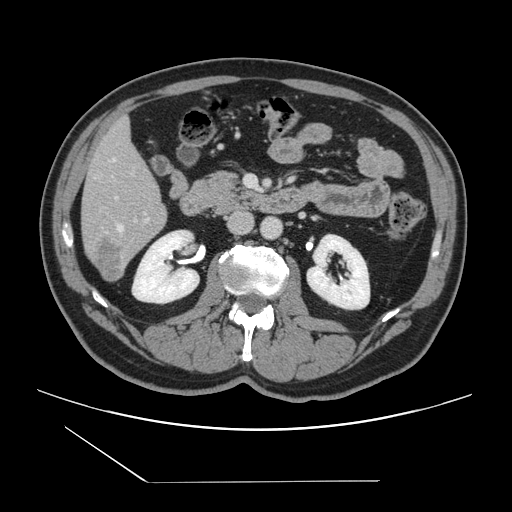
Contrast-enhanced abdominal CT, one axial slice. Position 52 of 157 along the scan axis. 120 kVp. Soft-tissue window (W 400 / L 40 HU). 512 × 512 image matrix, field of view 407 × 407 mm. Male patient, age 61 years. From the clinical record (not read from this slice): diagnosis: colorectal cancer liver metastases, imaged before liver resection; multiple liver metastases: yes; largest metastasis: 5.5 cm; disease in both lobes: yes.
Outlined on this slice (outlined manually by an expert reader):
- hepatic veins: box from (x=112, y=159) to (x=124, y=231) px
- liver: (x=82, y=120)–(x=167, y=280)
- planned liver remnant (the part of the liver to remain after resection): (x=83, y=120)–(x=163, y=218)
- portal vein (with intrahepatic branches): (x=115, y=197)–(x=149, y=221)
- liver metastasis: (x=93, y=239)–(x=126, y=278)